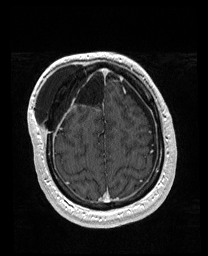
Brain MRI from a brain-tumour surgery series, one axial slice; slice 47 of 176 in the series (ordered by position); T1-weighted post-contrast; 1 mm slice thickness; 208 × 256 image matrix. From the clinical record (not read from this slice): histopathology: Astrocytoma; WHO grade: 4; IDH mutation: yes; tumour location: Right Orbitofrontal Anterior Temporal Insular.
Annotated regions visible in this slice (manually delineated by an expert):
- previous resection cavity: bounding box (x1, y1, x2, y2) in pixels: (56, 67, 106, 106)